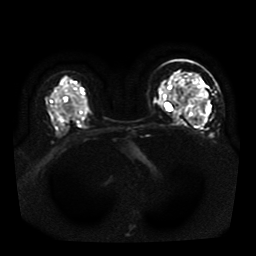
Breast MRI, one axial slice. Position 26 of 41 along the scan axis. Diffusion-weighted series; image 2 of 4 stored at this slice position (different b-values; order by instance number). 1.5 T. 5 mm slice thickness. 256 × 256 image matrix, field of view 330 × 330 mm. Female patient.
Structures marked on this image (manually delineated by an expert):
- tumour on diffusion-weighted imaging: bounding box [x1, y1, x2, y2] px = [202, 99, 207, 113]